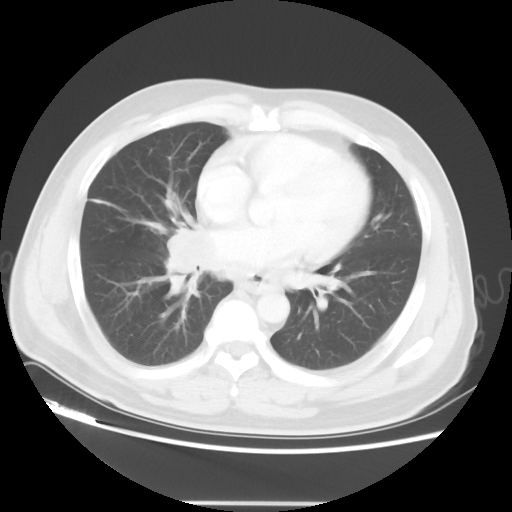
Chest CT, one axial slice. Reconstruction kernel STANDARD. 120 kVp. Lung window (W 1500 / L -600 HU). 512 × 512 image matrix, field of view 390 × 390 mm. Patient: male, 53 years. From the clinical record (not read from this slice): clinical TNM (as recorded): T2 N3 M0; histopathological grade: G3.
Structures marked on this image (rectangle marked by the reading radiologist):
- lung tumour (recorded histology: small cell carcinoma): bounding box [x1, y1, x2, y2] px = [150, 218, 211, 300]